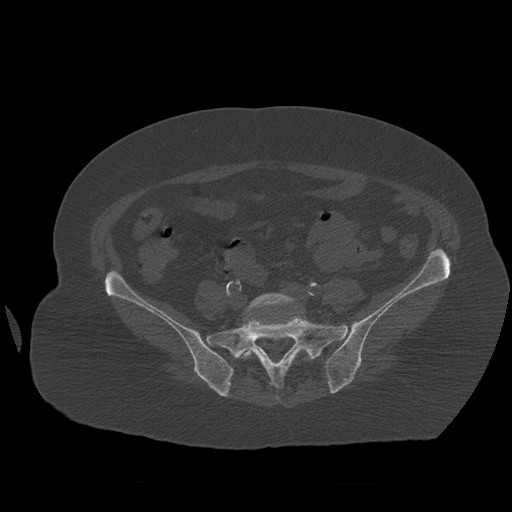
CT including the spine, one axial slice. Slice 169 of 399 in the series (ordered by position). 120 kVp. Bone window (W 1800 / L 400 HU). 1.25 mm slice thickness. 512 × 512 image matrix, field of view 404 × 404 mm. Patient age 81 years. Case-level facts recorded for this patient, not image findings: primary cancer: renal.
Structures marked on this image (semi-automatic segmentation, software-assisted and operator-edited):
- L5 vertebra: bounding box <243,293,296,360> (left, top, right, bottom; pixels)